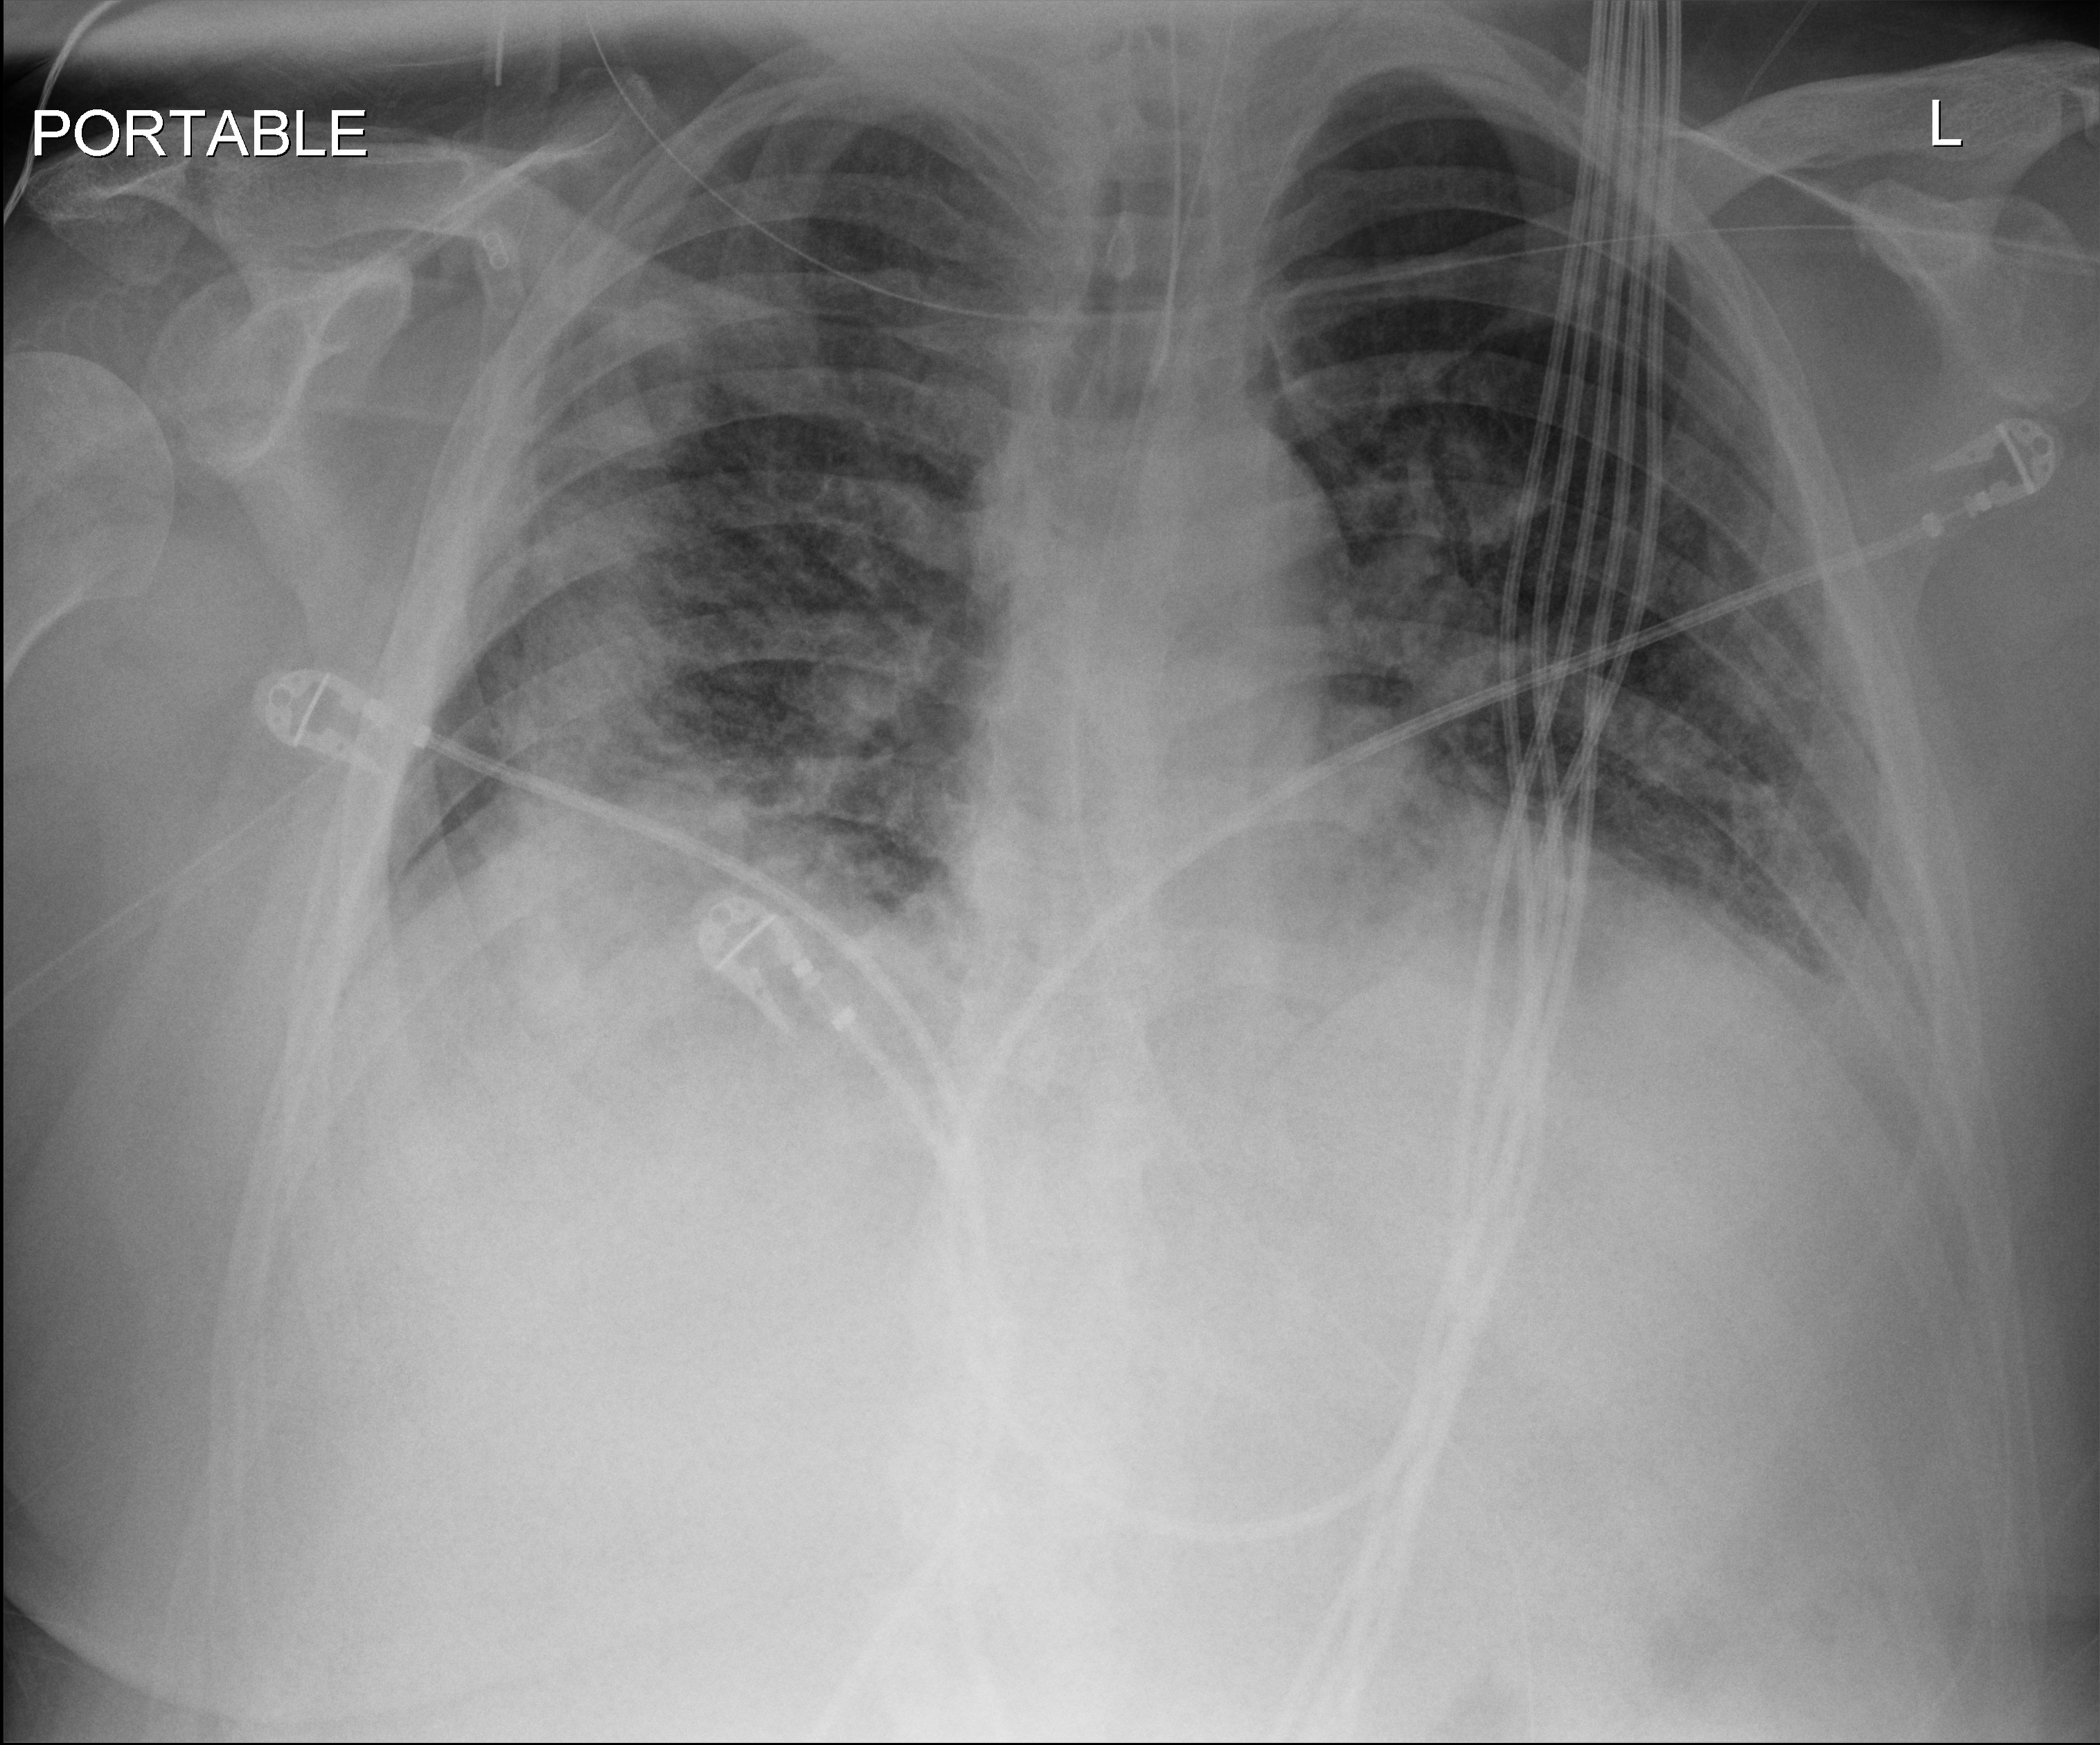
Chest X-ray (portable). Male patient hospitalised with COVID-19, age 18–59 years.
Hospital-stay facts (about this admission, not read from this image; timing relative to this image not recorded):
- mechanically ventilated during this hospital stay: yes
- other chronic lung disease (admission record): no